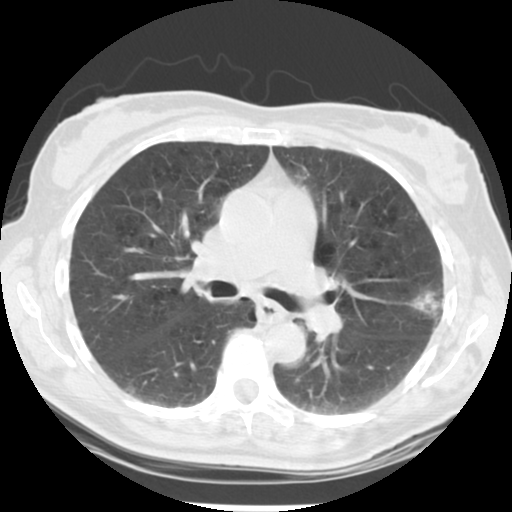
Low-dose screening chest CT, one axial slice; slice 131 of 223 in the series (ordered by position); reconstruction kernel STANDARD; lung window (W 1500 / L -600 HU); 2.5 mm slice thickness; 512 × 512 image matrix, field of view 302 × 302 mm.
Annotated regions visible in this slice (expert manual segmentation):
- lesion 1 (tumor, upper lobe of left lung): bounding box (x1, y1, x2, y2) in pixels: (412, 293, 442, 317)